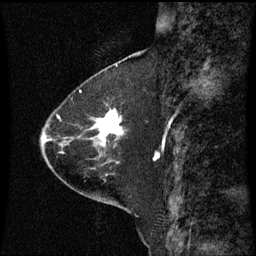
Breast MRI (dynamic contrast-enhanced), one sagittal slice; slice 23 of 60 in the series (ordered by position); dynamic contrast-enhanced series, image 2 of 3 at this slice position (ordered by acquisition); 1.5 T; TE 4.2 ms, TR 8.9 ms; 2 mm slice thickness; 256 × 256 image matrix, field of view 200 × 200 mm. Patient: female, 63 years. From the clinical record (not read from this slice): setting: breast cancer imaged before/during neoadjuvant chemotherapy; receptor status: HR-positive, HER2-negative.
Annotated regions visible in this slice (semi-automatic segmentation, software-assisted and operator-edited):
- analysis volume of interest (the breast-tissue region the enhancement analysis was run in; not a lesion): box from (x=78, y=104) to (x=124, y=149) px
- tumour enhancement mask (voxels above the 70 % enhancement threshold inside the analysis volume of interest): (x=95, y=110)–(x=123, y=145)